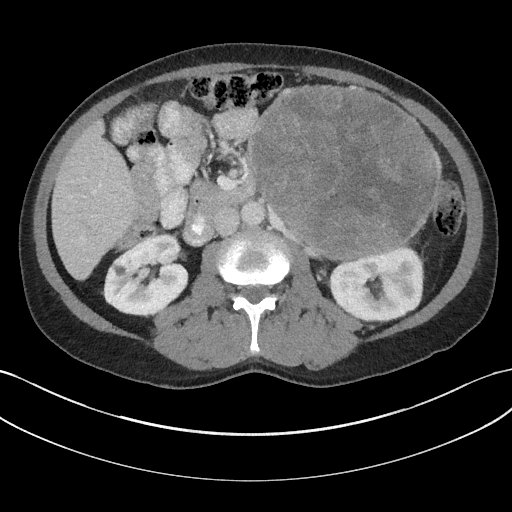
Contrast-enhanced abdominal CT, one axial slice; reconstruction kernel I31f/3; 100 kVp; intravenous contrast given; soft-tissue window (W 400 / L 40 HU); 512 × 512 image matrix, field of view 384 × 384 mm. Patient: male, 58 years. From the clinical record (not read from this slice): diagnosis: adrenocortical carcinoma; tumour side: left adrenal; tumour size at pathology: 22 cm; Ki-67 index: 26 %; stage (as recorded): 2.
Annotated regions visible in this slice (semi-automatic segmentation, software-assisted and operator-edited):
- mass: bounding box (x1, y1, x2, y2) in pixels: (252, 86, 438, 259)